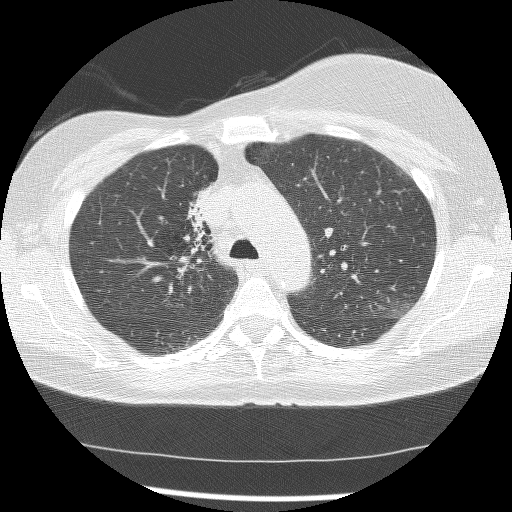
Axial slice from a low-dose chest CT screening exam; first (baseline) screen; lung window (W 1500 / L -600 HU); slice 45 of 172 in the series; 512 × 512 image matrix. Female, age 56 years at enrolment. Current smoker at enrolment.
- Lesion marked by an expert reader, bounding box (x1, y1, x2, y2) in pixels: (164, 180, 221, 268).
- The screening reader recorded 2 non-calcified nodules or masses ≥4 mm on this exam (right lower lobe, right middle lobe); which of them this box marks is not recorded.